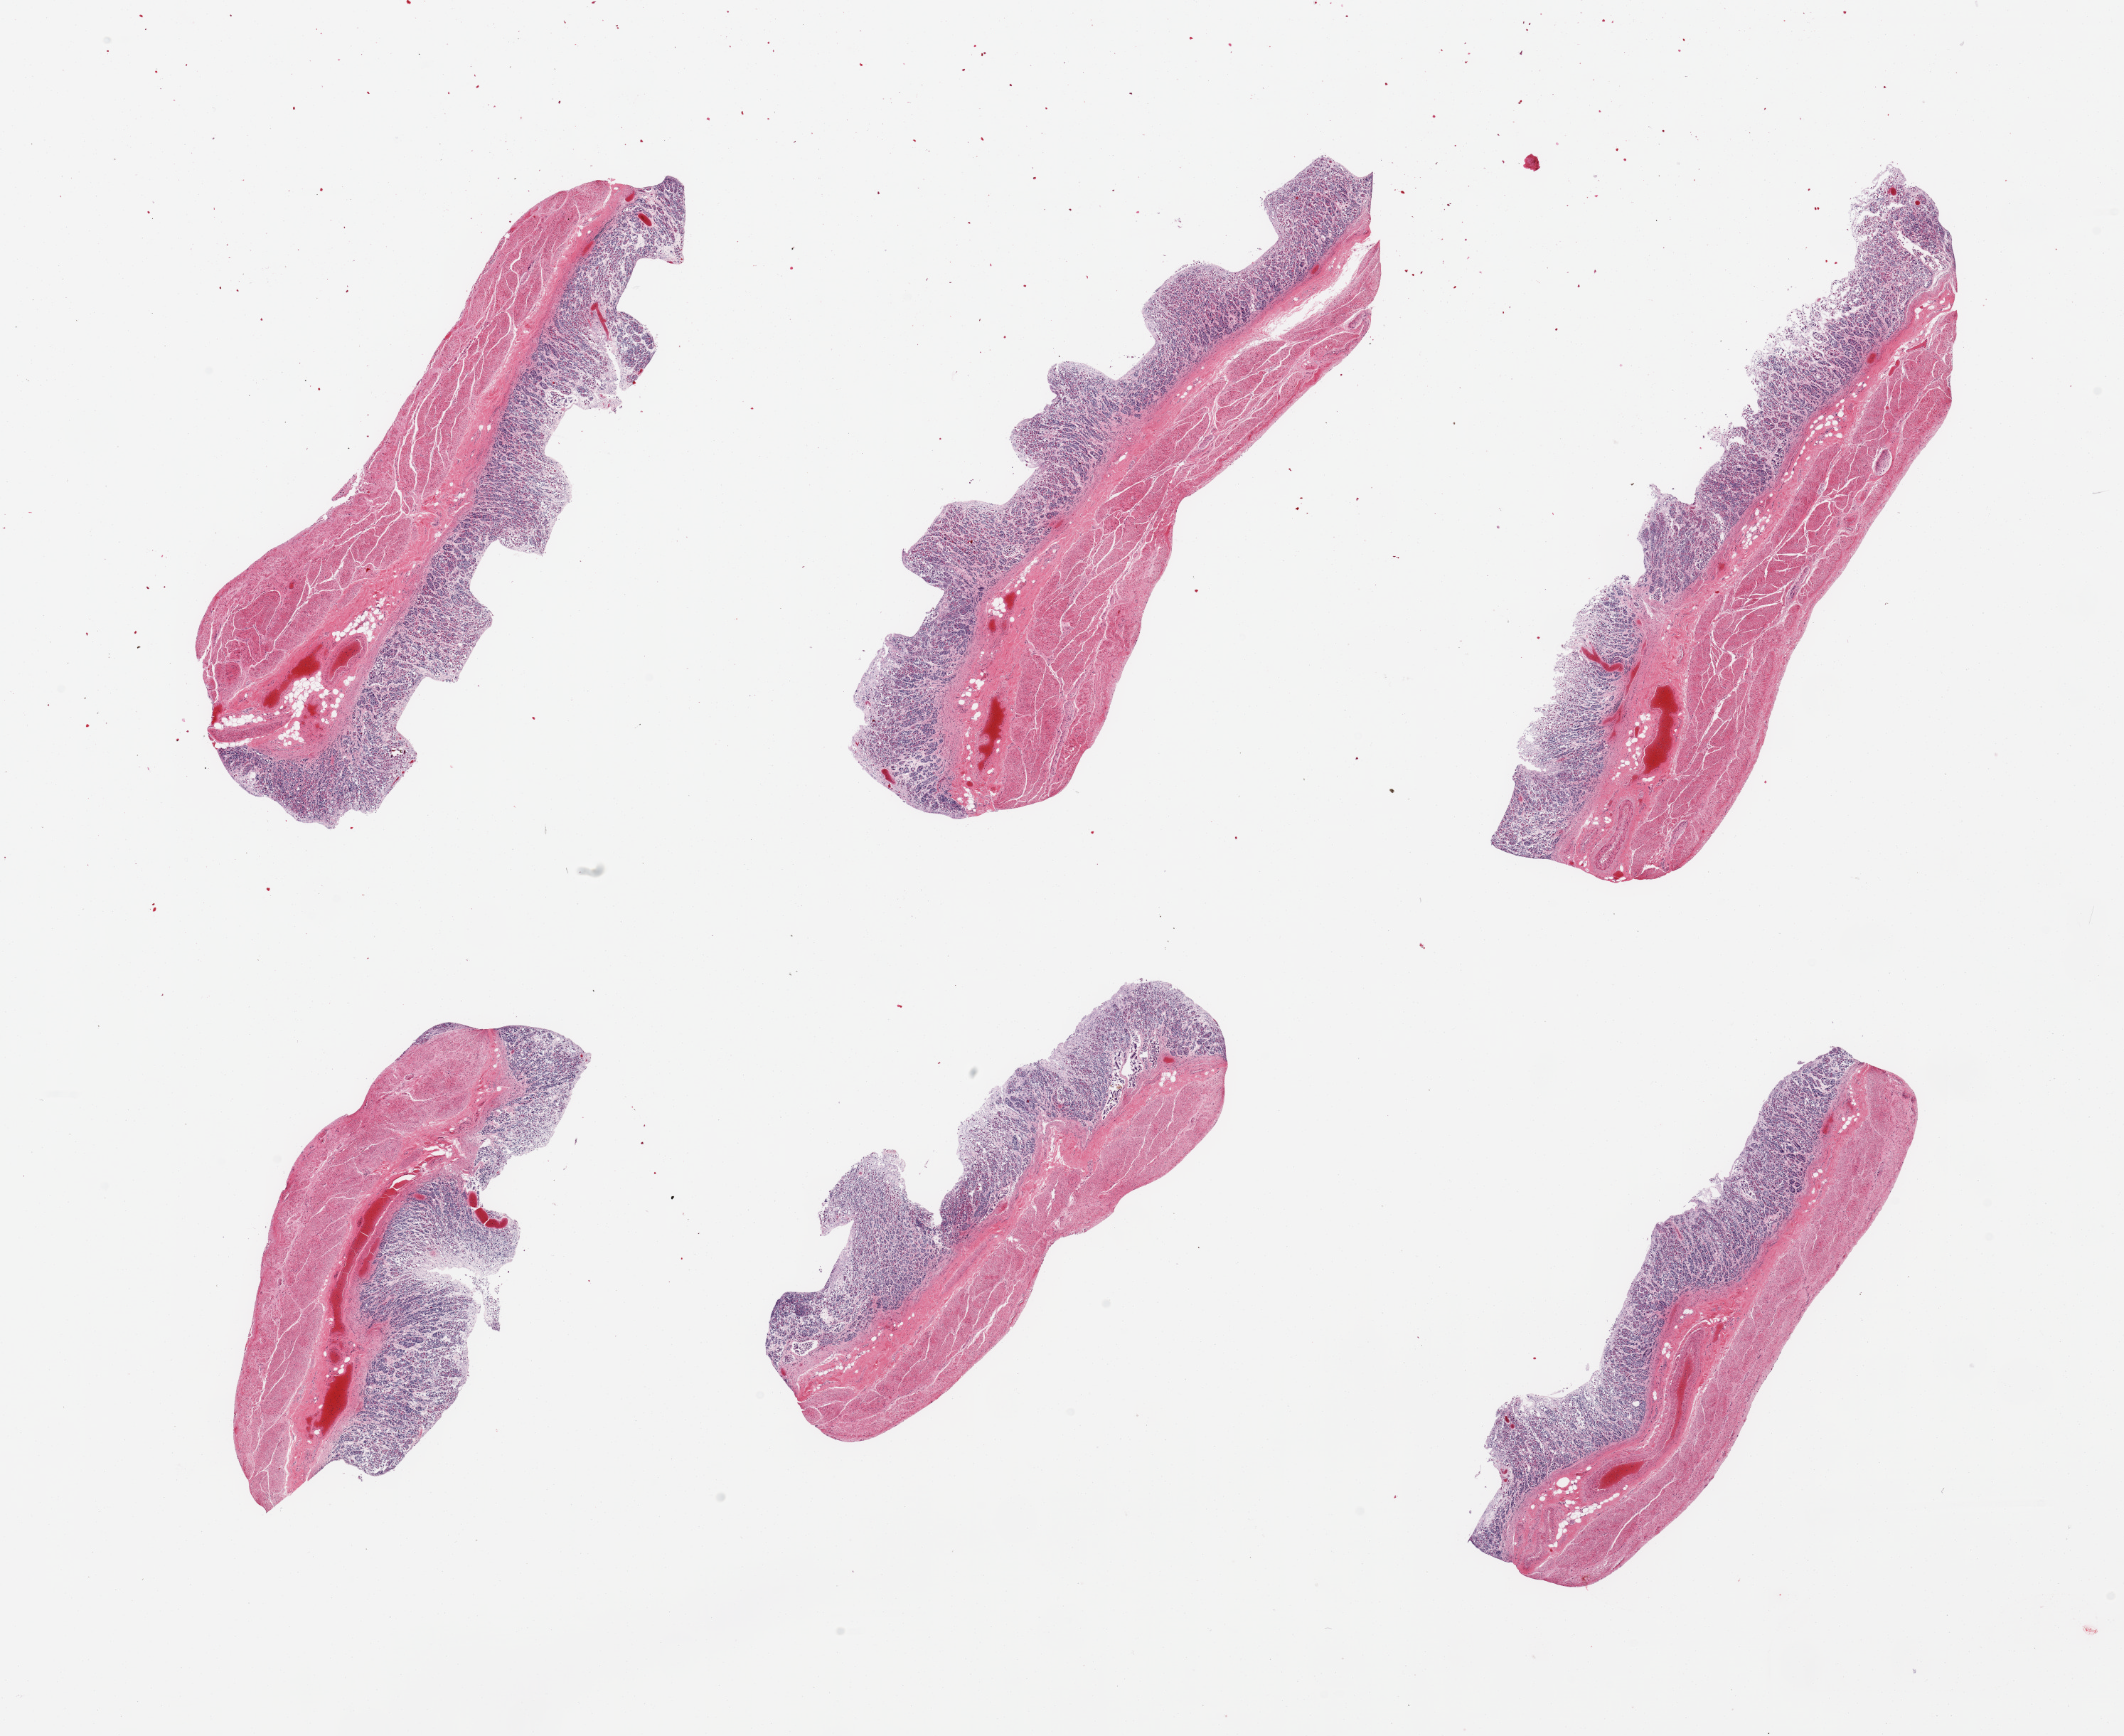
Whole-slide image, H&E stain — whole scanned area (about 23.6 x 19.3 mm) shown as a low-resolution overview. PAXgene-fixed, paraffin-embedded tissue. Target tissue: stomach. Tissue donor sample. Donor: male.
Reviewer comment on this tissue sample: 6 pieces; full thickness.